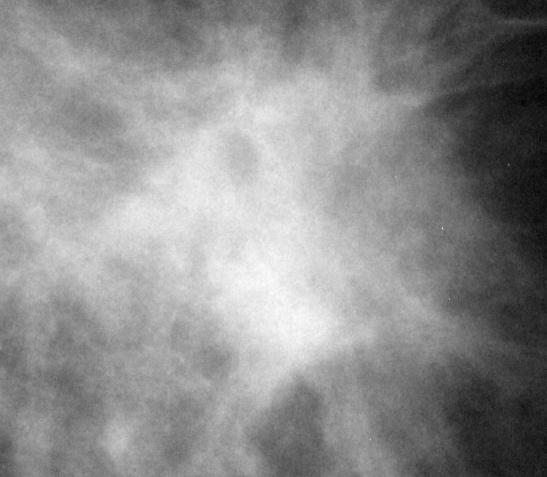
Region of interest cut from a scanned film mammogram (one marked finding), right breast, MLO view.
- Marked abnormality: mass, shape irregular, margins spiculated; BI-RADS assessment category 5; pathology (as recorded): malignant.